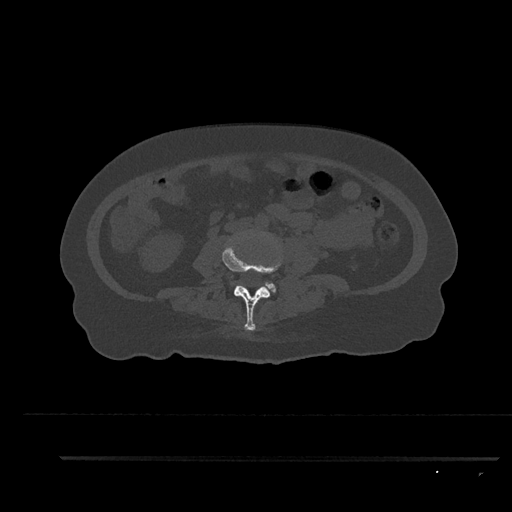
CT including the spine, one axial slice. Position 66 of 797 along the scan axis. Reconstruction kernel Br40s/3. 120 kVp. Bone window (W 1800 / L 400 HU). 512 × 512 image matrix. Female patient, age 44 years. From the clinical record (not read from this slice): primary cancer: renal; vertebrae with lytic lesions (as recorded): L1.
Outlined on this slice (semi-automatic segmentation, software-assisted and operator-edited):
- L3 vertebra: bounding box (x1, y1, x2, y2) in pixels: (222, 241, 281, 331)
- L4 vertebra: (262, 282, 276, 293)